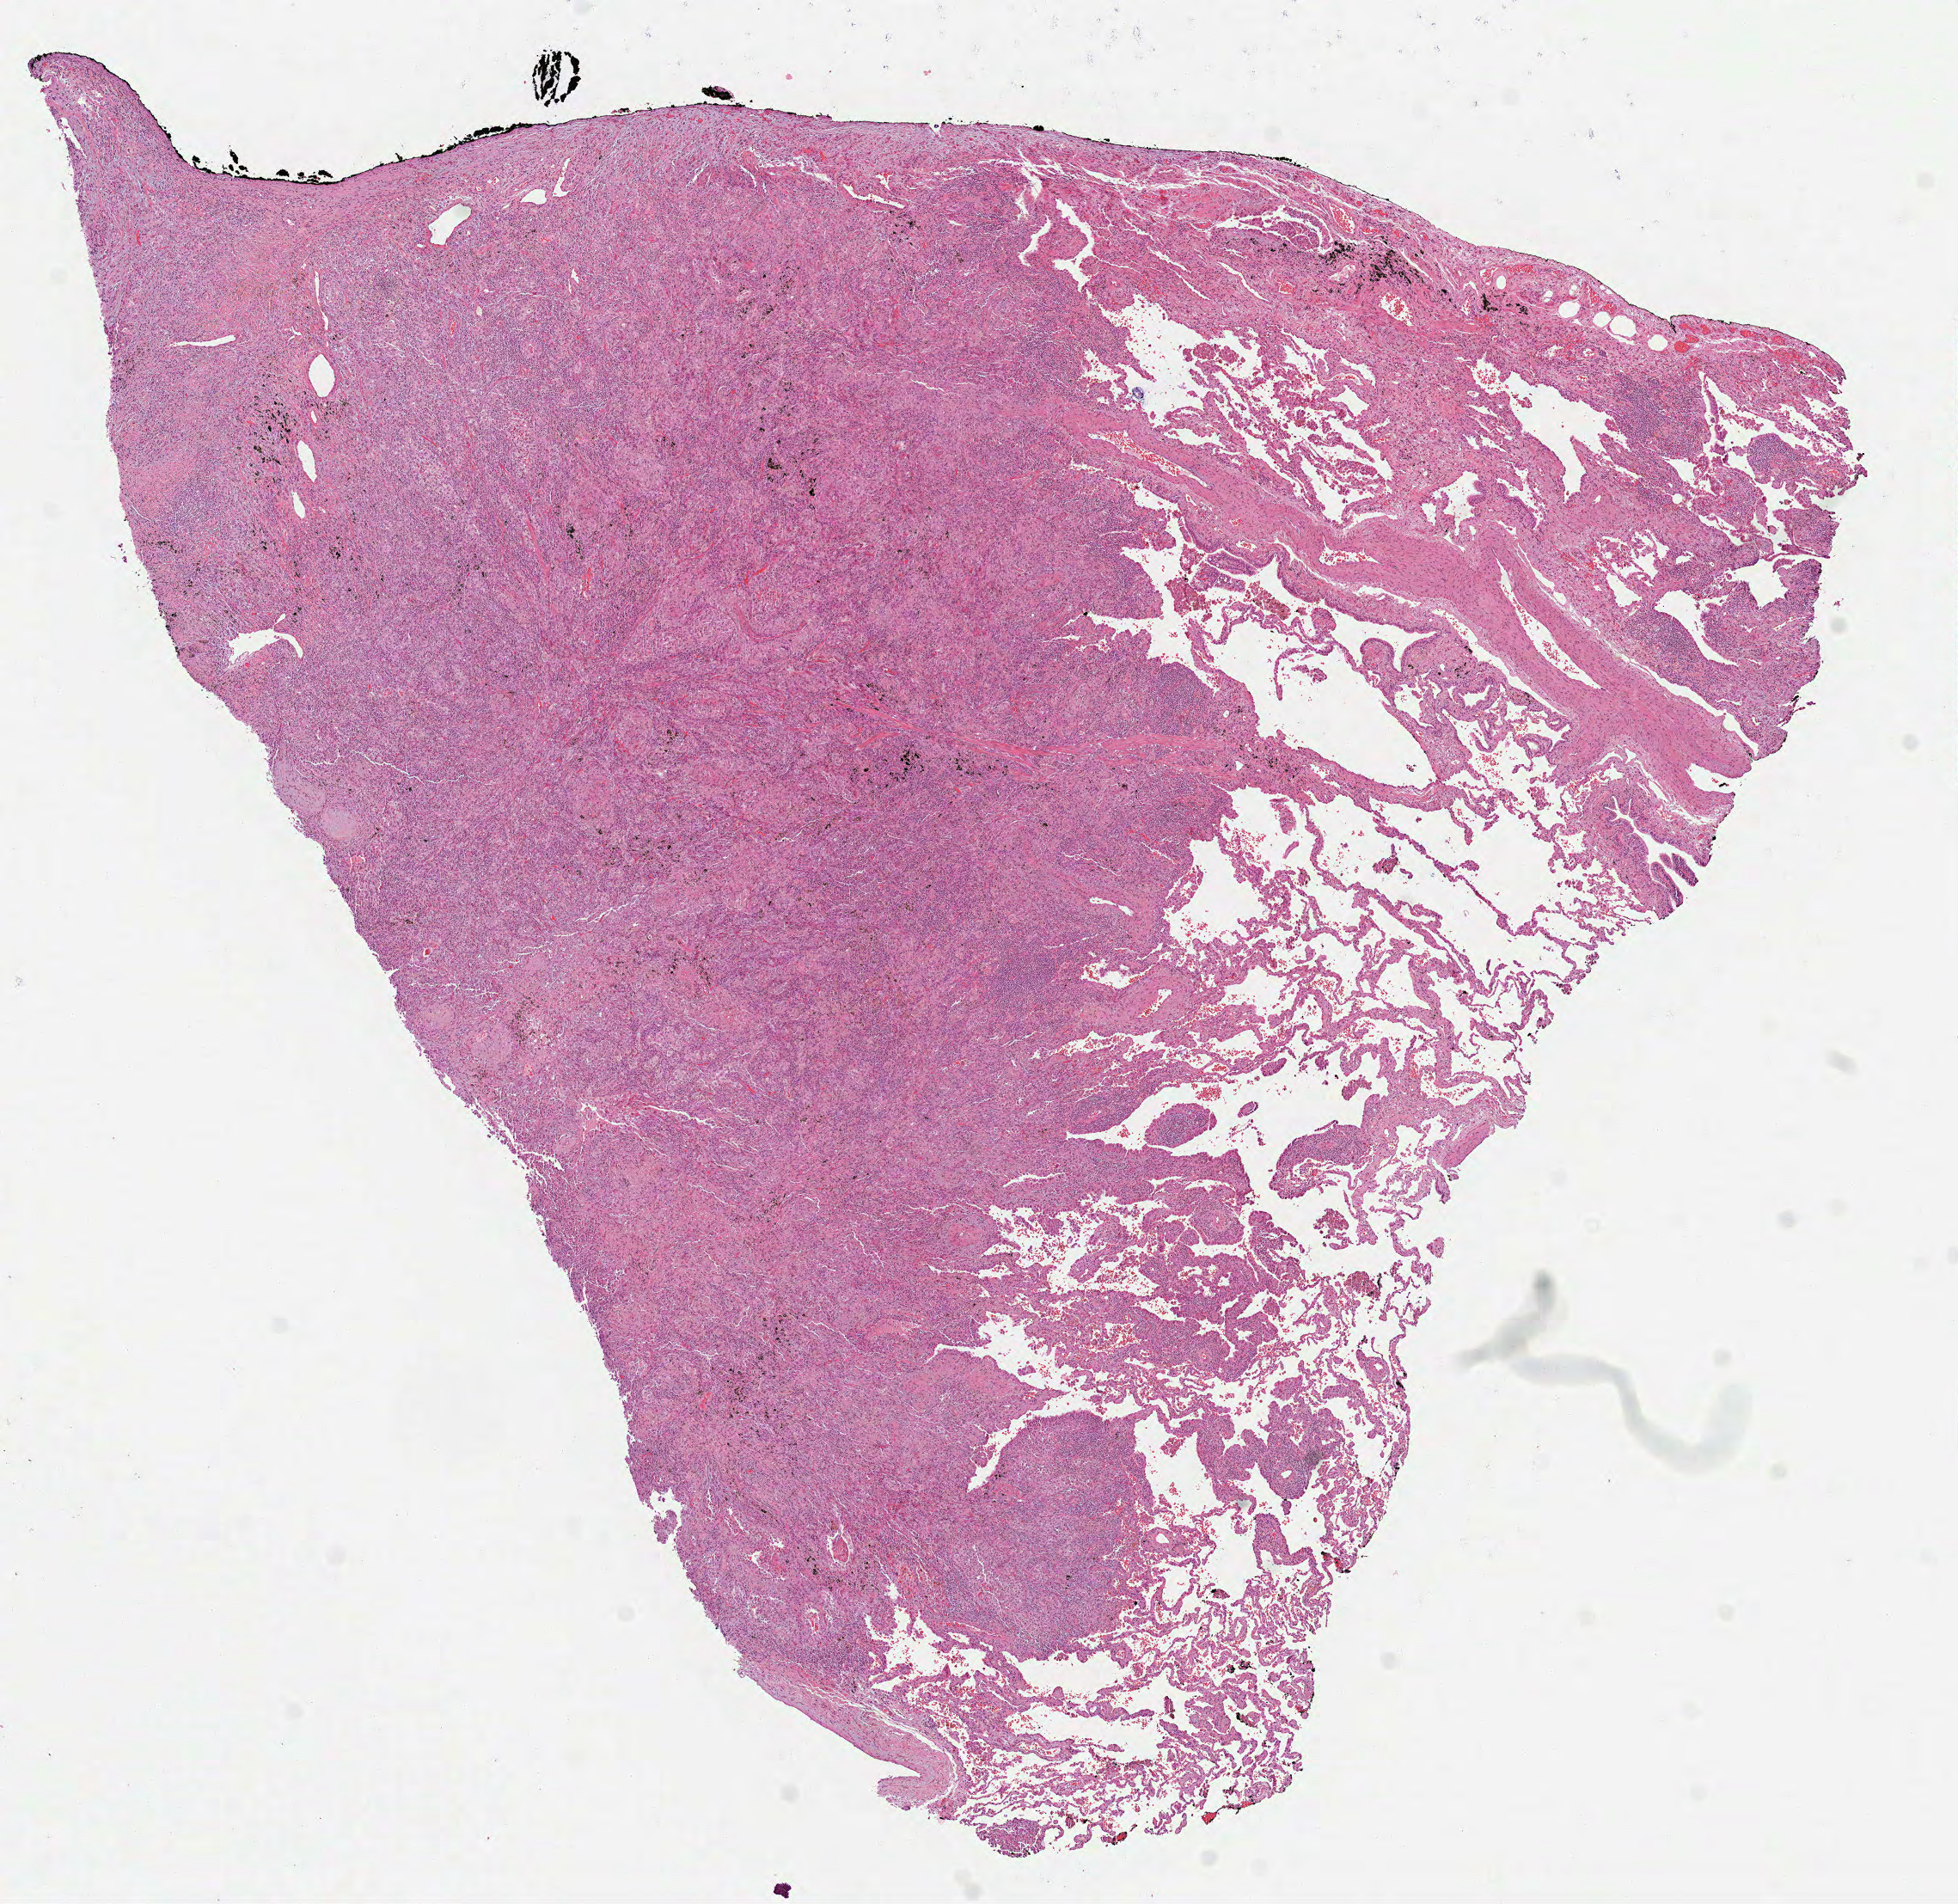
Hematoxylin and eosin (H&E) stained whole-slide image — shown as a low-resolution overview of the whole scanned area (about 9.2 x 8.9 mm), formalin-fixed paraffin-embedded (FFPE) diagnostic section, lung, primary tumour sample. Patient: female, age at initial diagnosis 75 years.
Histologic diagnosis: Adenocarcinoma, NOS (lower lobe, lung).